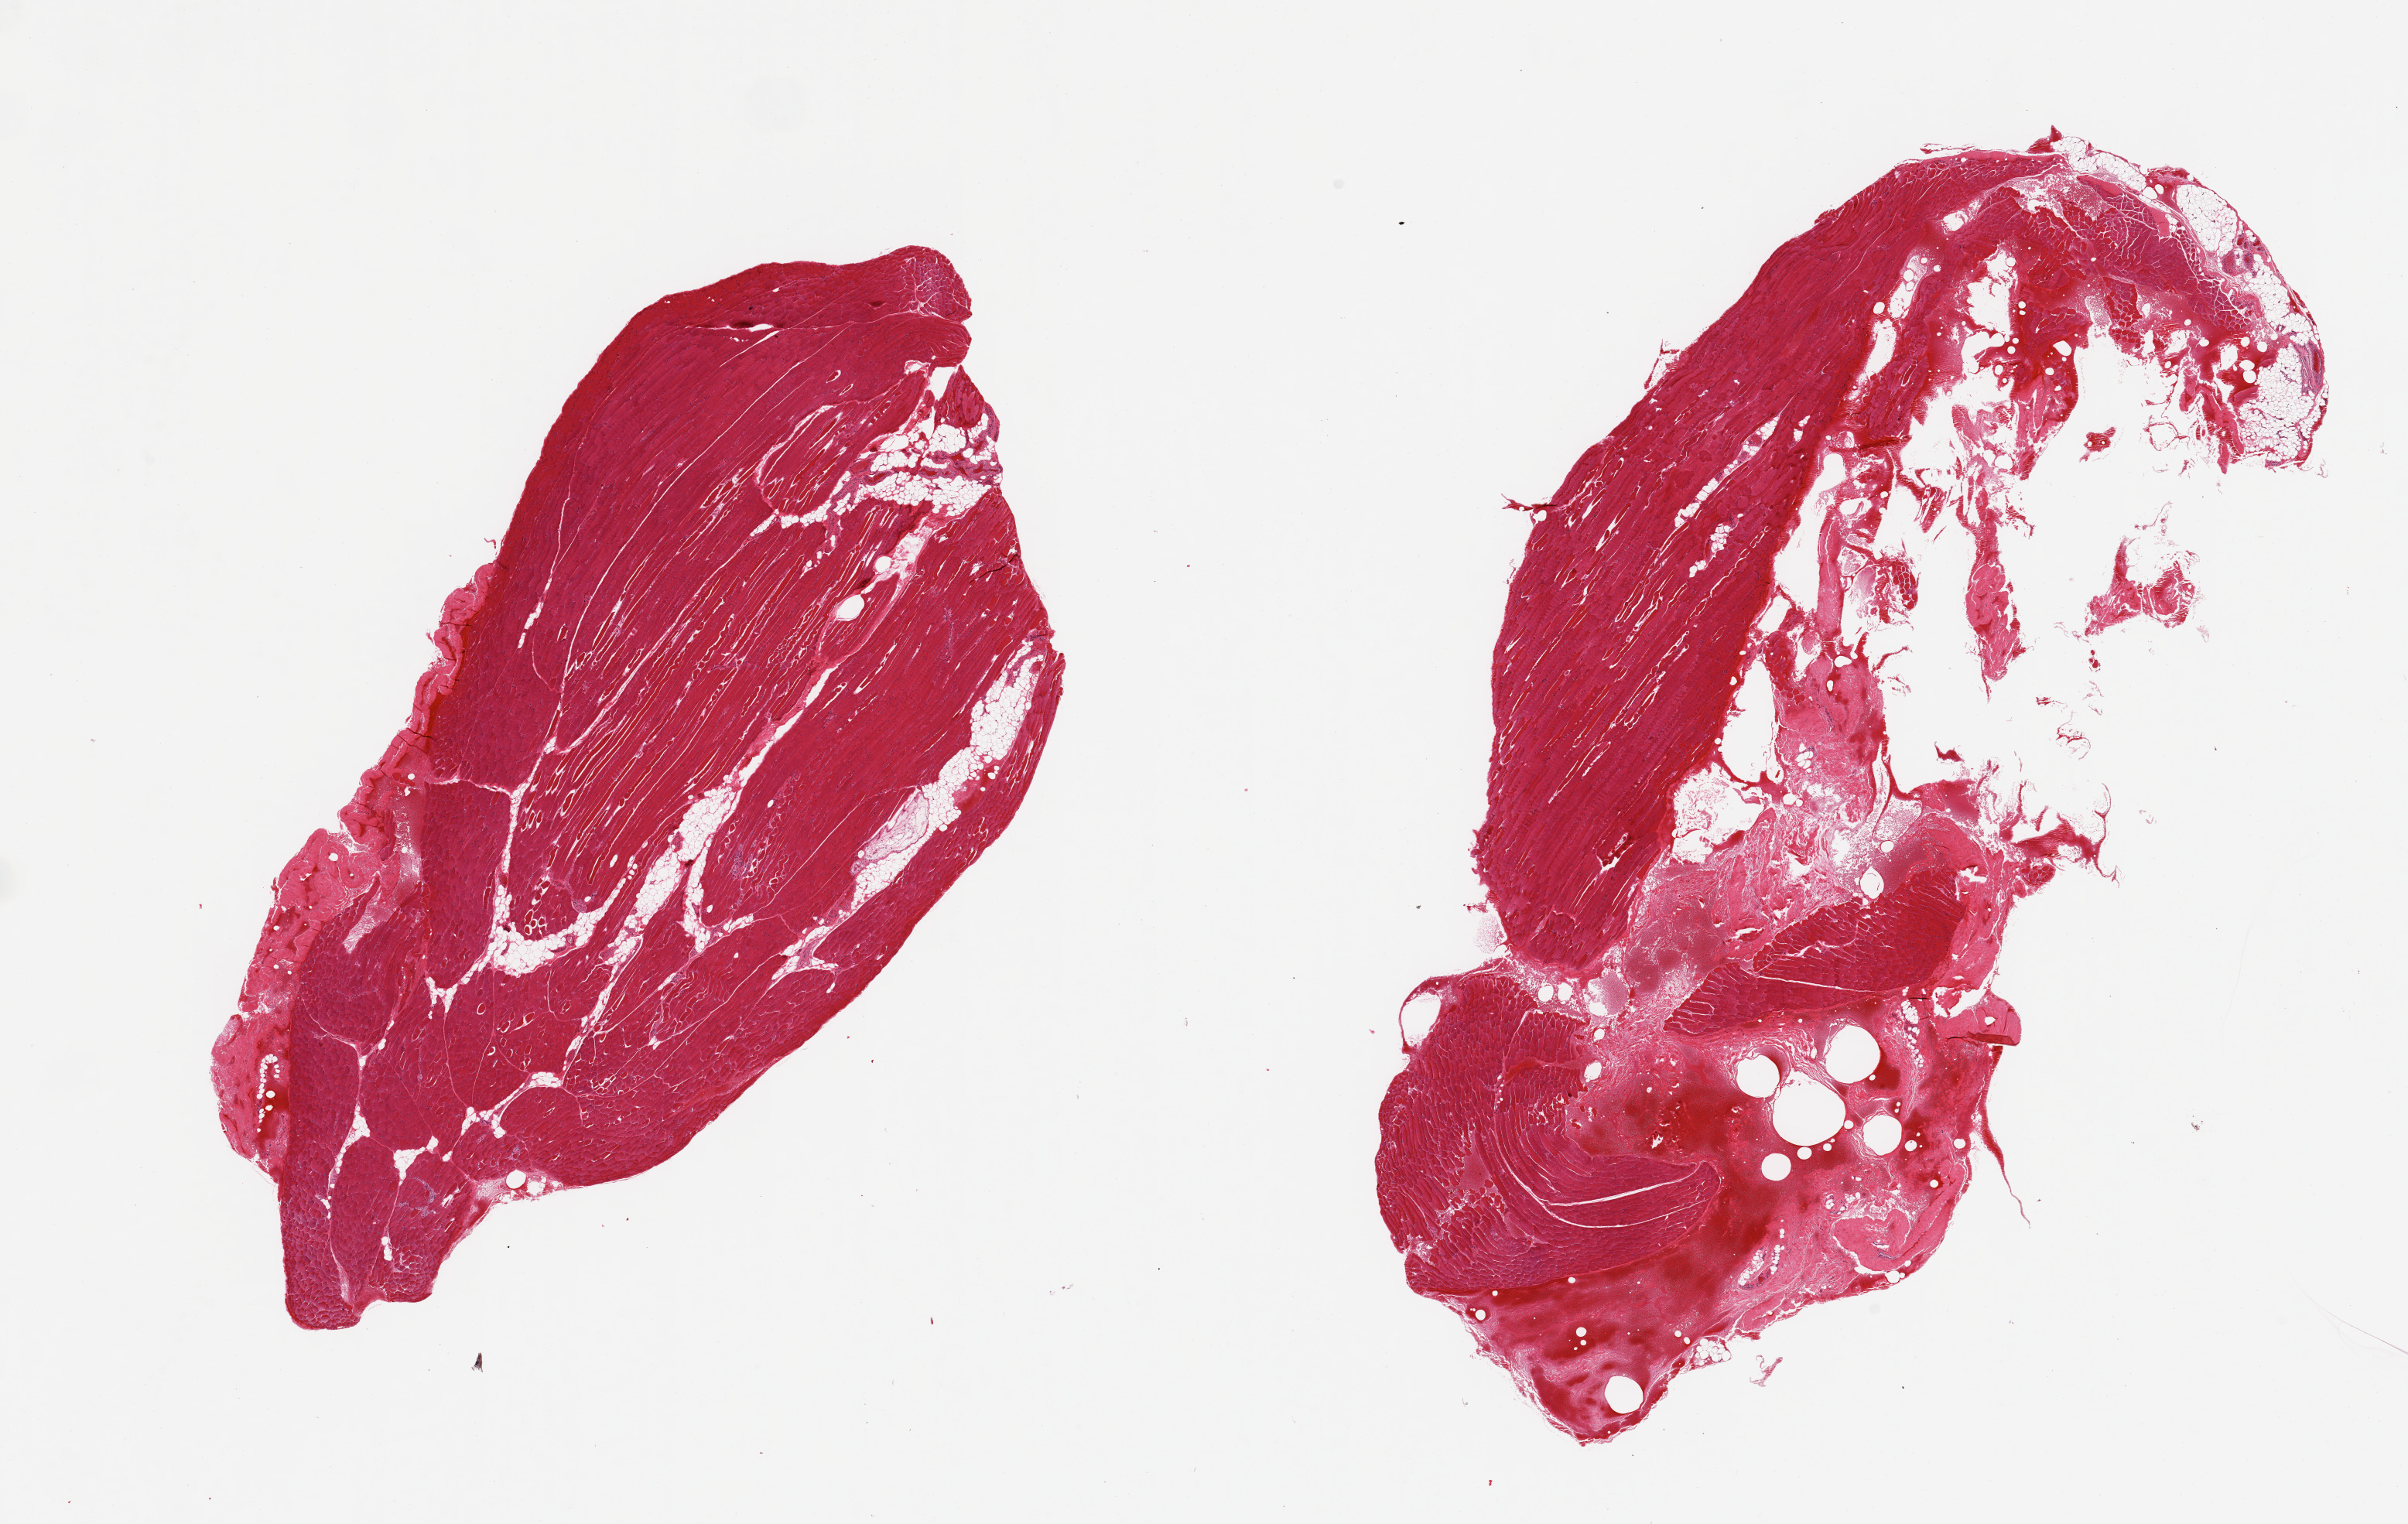
Haematoxylin and eosin whole-slide image — whole scanned area (about 24.6 x 15.6 mm, slide scanned at 20x) shown as a low-resolution overview; PAXgene-fixed paraffin-embedded (PFPE) section; section of skeletal muscle (target tissue); tissue donor sample. Donor sex: male.
Review note (as recorded): 2 pieces. 1 has large central fibroadipose component about 60%; other <10% fat.